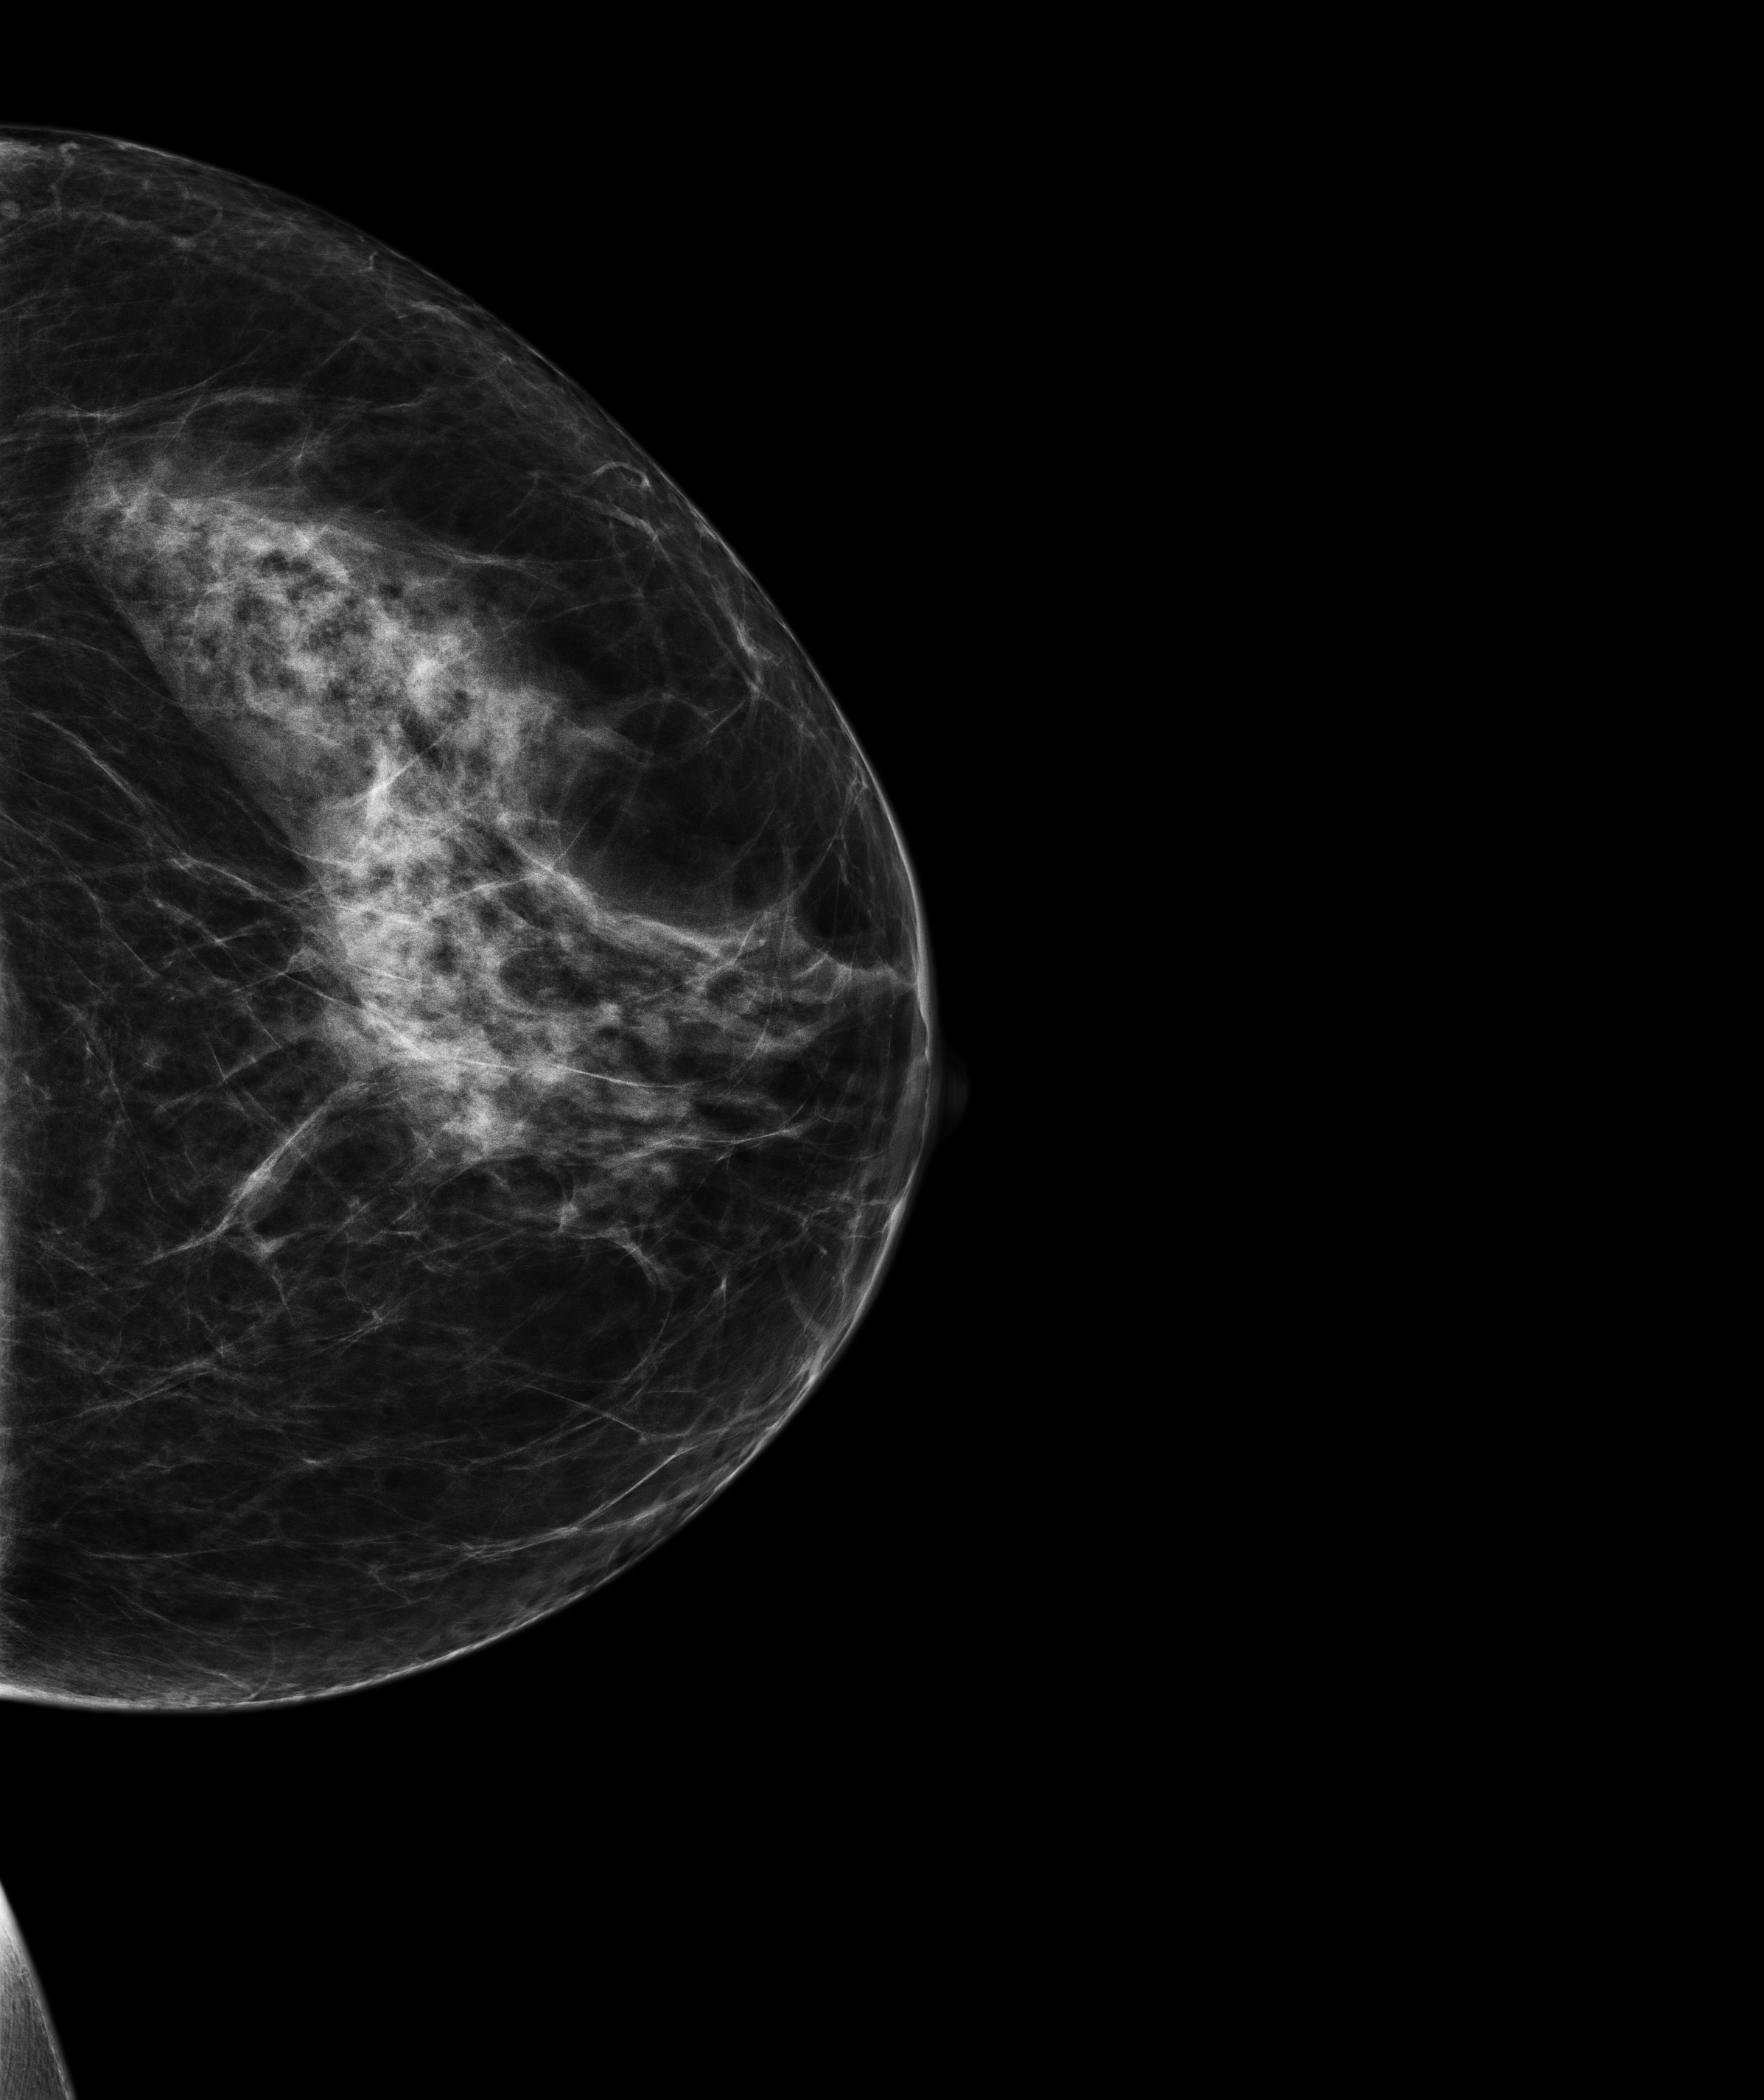
Full-field digital mammogram (FFDM); left breast; cranio-caudal projection; annual screening mammography examination; compressed breast thickness 61.6 mm; system: Senographe Pristina. Patient aged 56 years (female).
BI-RADS breast density category at the screening exam (both breasts, scale 1–4): 3. Final BI-RADS category for the screening round (tomosynthesis exam, both breasts): category 1. Recall: no recall after this screen.